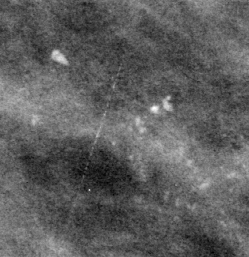
Region of interest cut from a scanned film mammogram (one marked finding), left breast, MLO view.
- Calcifications, morphology pleomorphic, distribution clustered; BI-RADS assessment category 4; pathology result (as recorded, not read from the image): malignant.